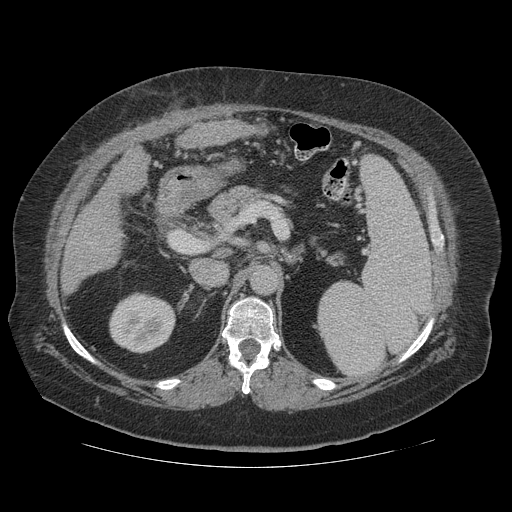
Contrast-enhanced abdominal CT (liver protocol), one axial slice; slice 62 of 121 in the series (ordered by position); reconstruction kernel STANDARD; 140 kVp; soft-tissue window (W 400 / L 40 HU); 2.5 mm slice thickness; 512 × 512 image matrix, field of view 420 × 420 mm. From the clinical record (not read from this slice): diagnosis: hepatocellular carcinoma (patient treated with transarterial chemoembolisation; whether this scan precedes or follows treatment is not stated here); TNM stage (as recorded): Stage-IIIA; Child-Pugh class: A; tumour nodularity: multinodular; tumour size: 7.4 cm.
Structures marked on this image (semi-automatic segmentation, software-assisted and operator-edited):
- liver parenchyma outside the tumour (the mass and vessels are separate outlines, so this box may not span the whole liver): bounding box <62,120,261,292> (left, top, right, bottom; pixels)